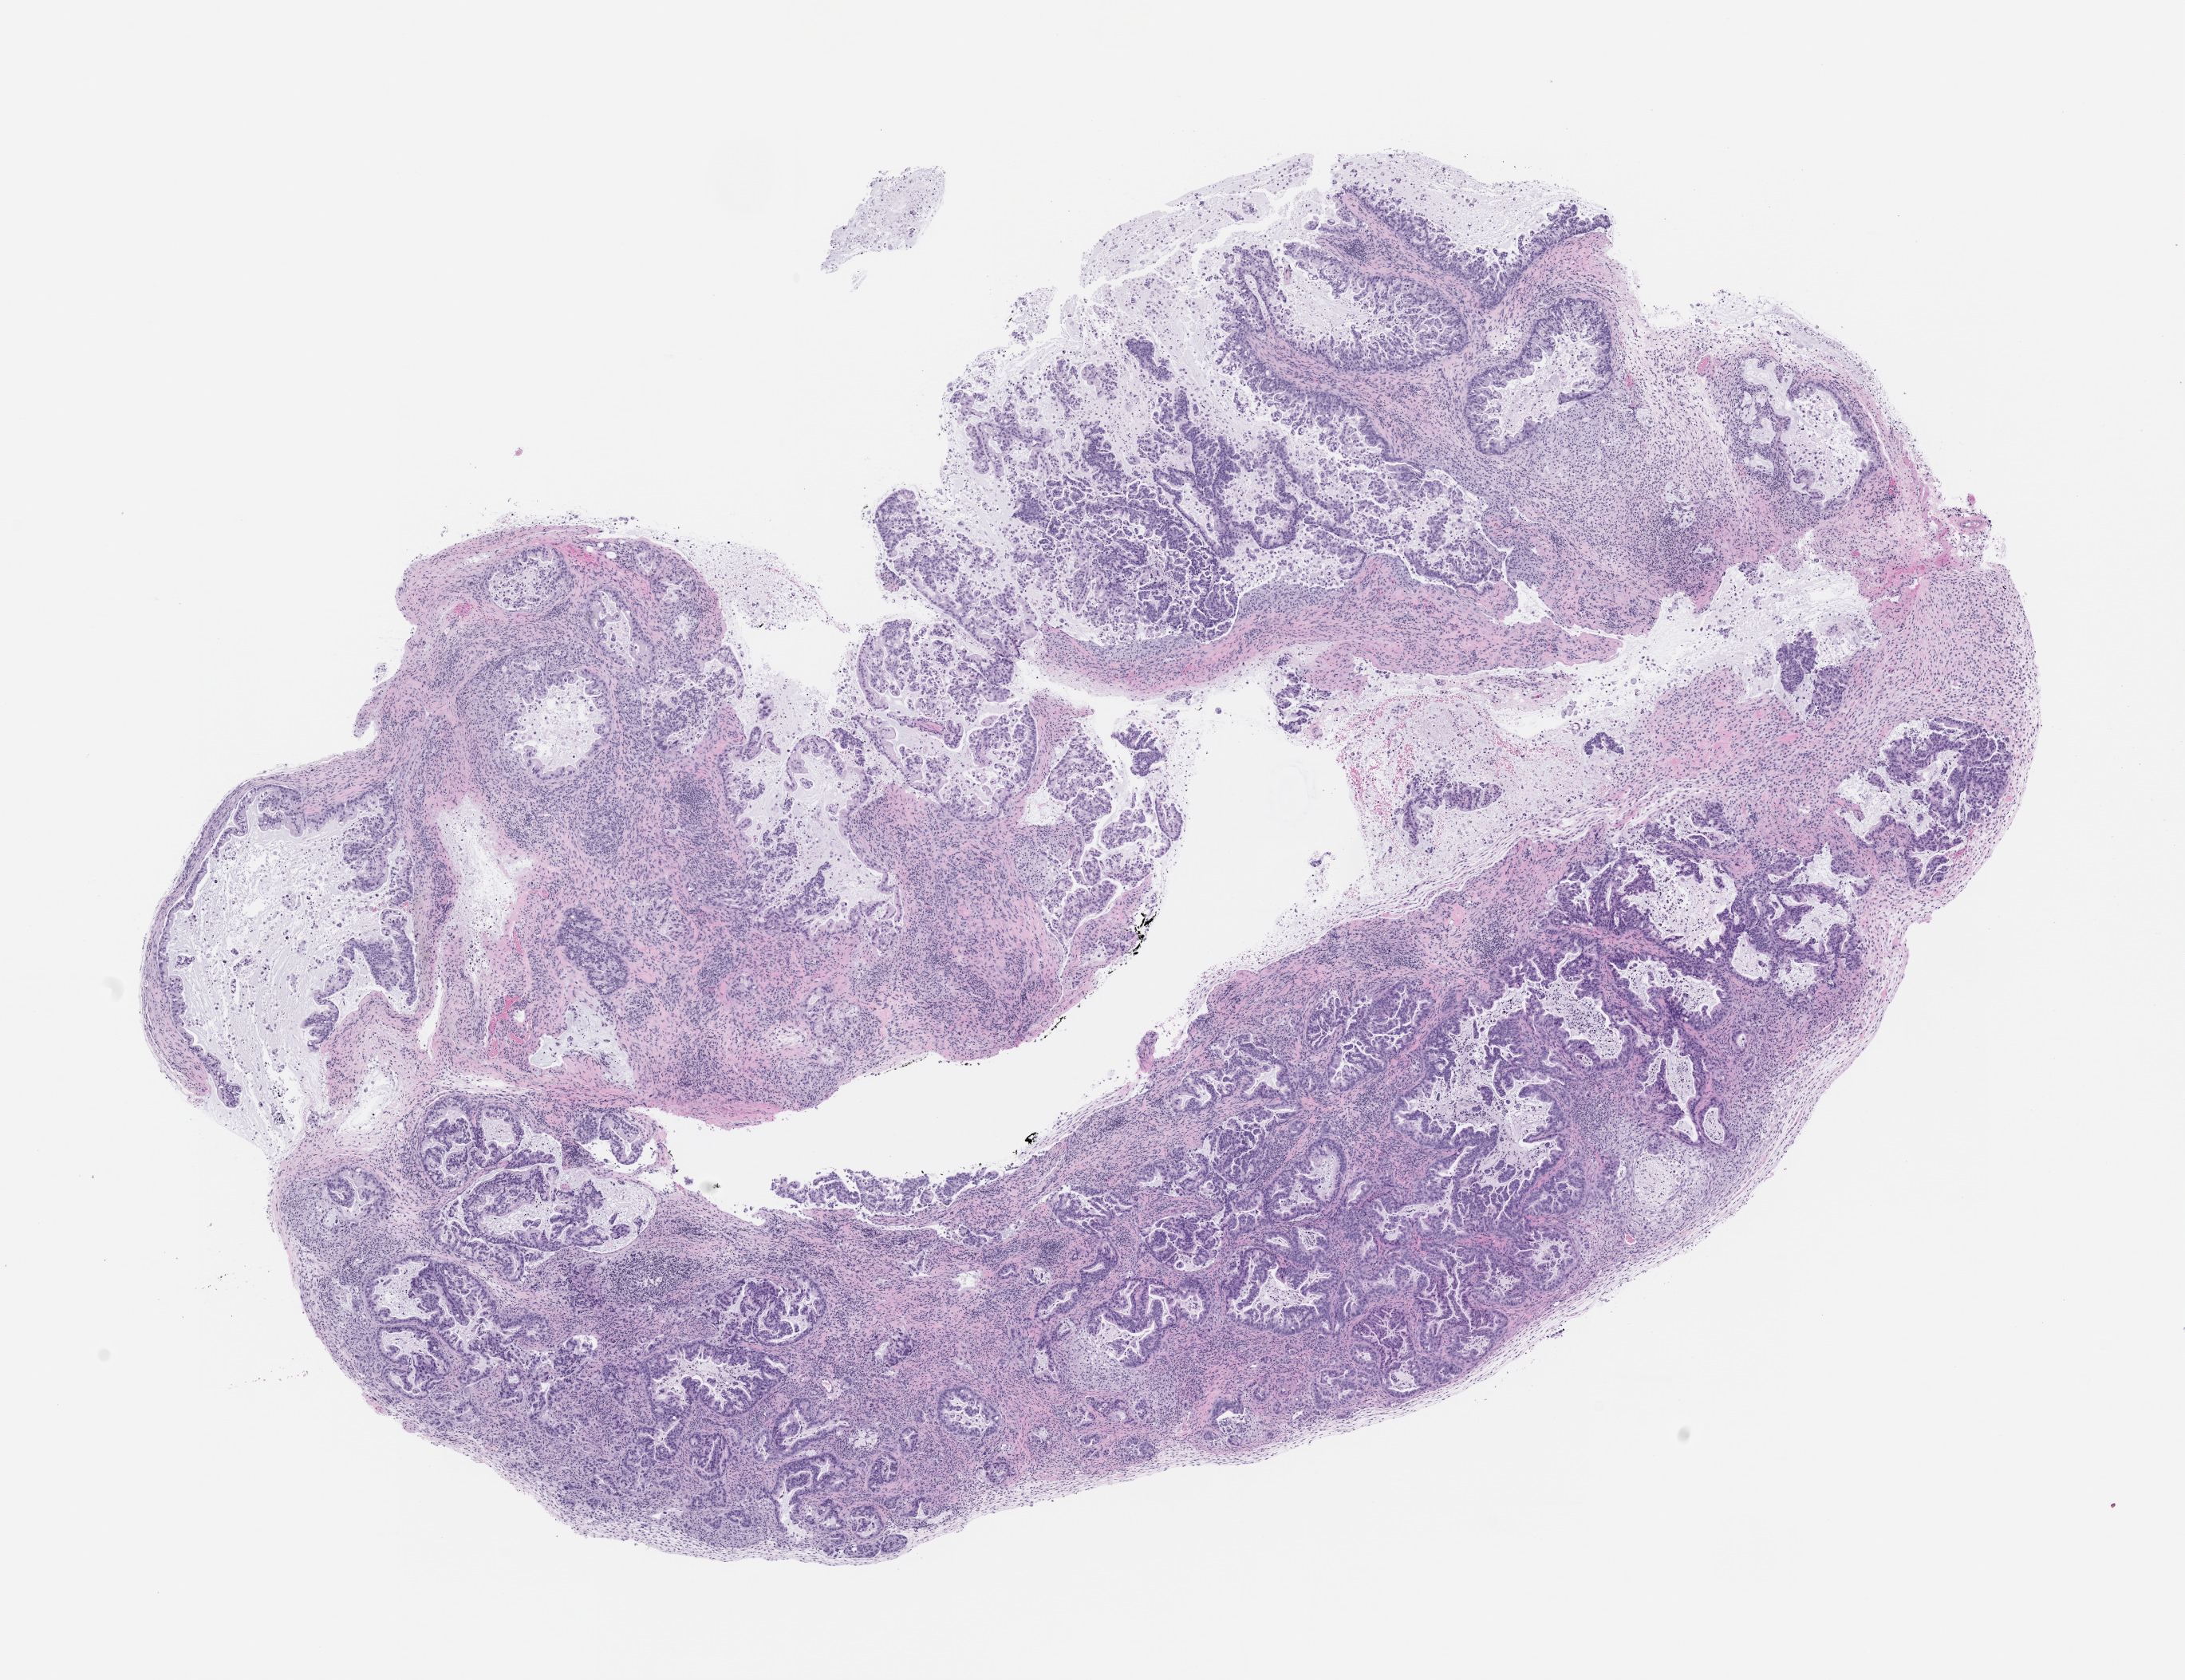
Haematoxylin and eosin whole-slide image of a patient-derived xenograft (PDX) tumor grown in a mouse, passage 2, a low-resolution overview of the entire scanned area, about 11.0 x 8.5 mm, formalin-fixed, paraffin-embedded (FFPE) tissue, tumor site category: pancreas.
Originating patient diagnosis: Pancreatic Adenocarcinoma.